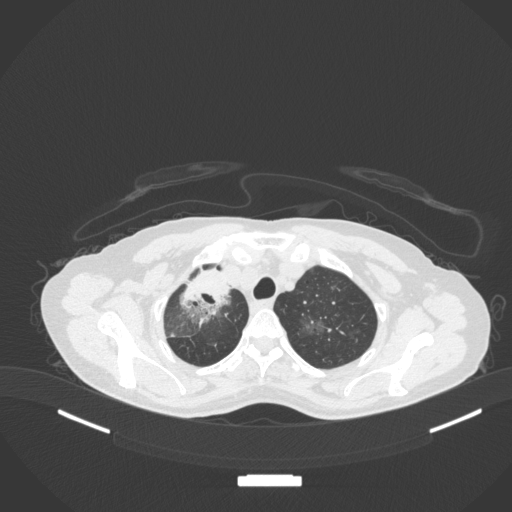
Chest CT, one axial slice; slice 275 of 311 in the series (ordered by position); lung window (W 1500 / L -600 HU); 1 mm slice thickness; 512 × 512 image matrix, field of view 400 × 400 mm. Patient: female, 59 years. Case-level facts recorded for this patient, not image findings: clinical TNM (as recorded): T3 N0 M0; histopathological grade: G1.
Structures marked on this image (bounding box drawn by a radiologist):
- lung tumour (recorded histology: adenocarcinoma): bounding box <177,264,234,325> (left, top, right, bottom; pixels)